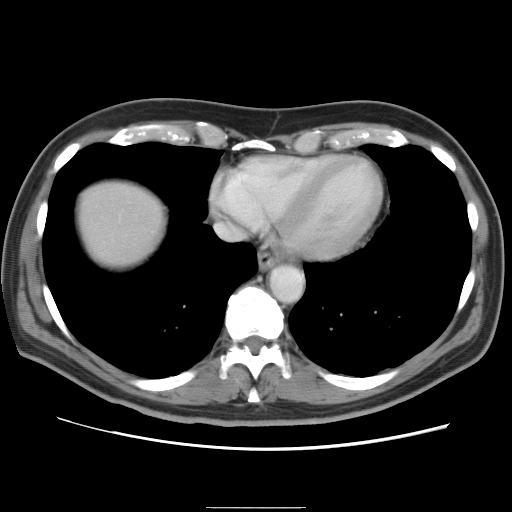
Contrast-enhanced abdominal CT, one axial slice. Position 80 of 87 along the scan axis. Intravenous contrast given. Soft-tissue window (W 400 / L 40 HU). 5 mm slice thickness. 512 × 512 image matrix, field of view 363 × 363 mm. Male patient, age 63 years. Case-level facts recorded for this patient, not image findings: diagnosis: colorectal cancer liver metastases, imaged before liver resection; multiple liver metastases: no; largest metastasis: 9 cm; disease in both lobes: no.
Annotated regions visible in this slice (expert manual segmentation):
- liver: bounding box <79,181,164,263> (left, top, right, bottom; pixels)
- planned liver remnant (the part of the liver to remain after resection): <80,188,164,263>